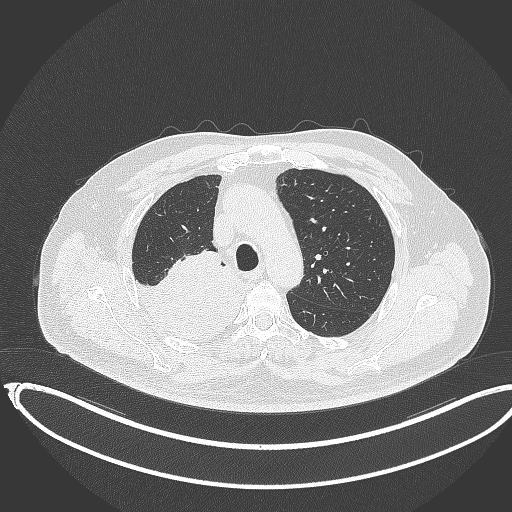
Chest CT, one axial slice. Slice 266 of 403 in the series (ordered by position). Reconstruction kernel B70f. Lung window (W 1500 / L -600 HU). 1 mm slice thickness. 512 × 512 image matrix, field of view 436 × 436 mm. Patient: male, 68 years. From the clinical record (not read from this slice): clinical TNM (as recorded): T2a N0 M0.
Annotated regions visible in this slice (rectangle marked by the reading radiologist):
- lung tumour (recorded histology: adenocarcinoma): box from (x=134, y=243) to (x=245, y=342) px